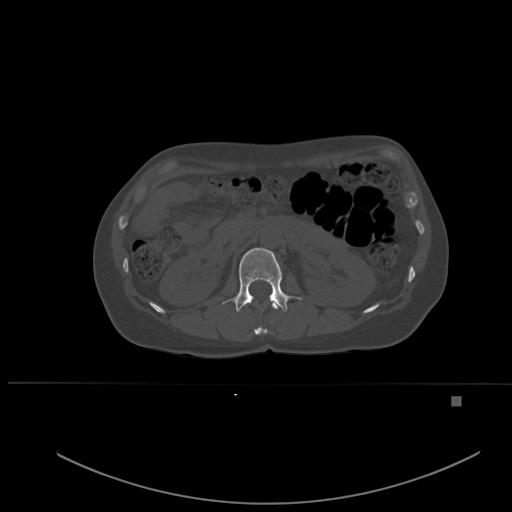
CT including the spine, one axial slice. Position 238 of 651 along the scan axis. Bone window (W 1800 / L 400 HU). 512 × 512 image matrix, field of view 443 × 443 mm. Female patient, age 49 years. Case-level facts recorded for this patient, not image findings: primary cancer: breast.
Structures marked on this image (semi-automatic segmentation, software-assisted and operator-edited):
- L1 vertebra: box from (x=222, y=248) to (x=302, y=312) px
- T12 vertebra: (x=243, y=303)–(x=278, y=335)